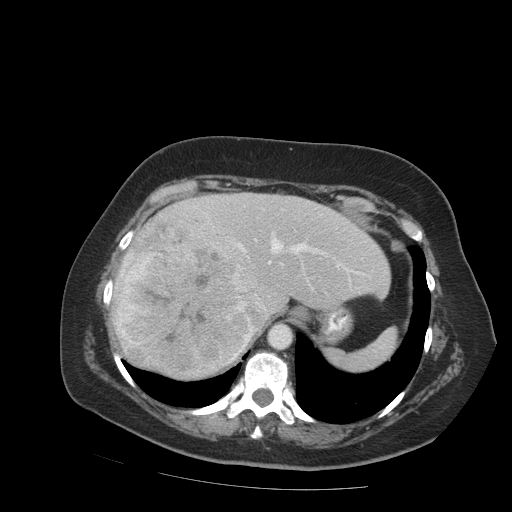
Contrast-enhanced abdominal CT (liver protocol), one axial slice. Slice 67 of 99 in the series (ordered by position). Reconstruction kernel STANDARD. Soft-tissue window (W 400 / L 40 HU). 512 × 512 image matrix, field of view 400 × 400 mm. Case-level facts recorded for this patient, not image findings: diagnosis: hepatocellular carcinoma (patient treated with transarterial chemoembolisation; whether this scan precedes or follows treatment is not stated here); TNM stage (as recorded): Stage-IVB; Child-Pugh class: A.
Structures marked on this image (semi-automatic segmentation, software-assisted and operator-edited):
- abdominal aorta: bounding box (x1, y1, x2, y2) in pixels: (268, 324, 292, 348)
- liver parenchyma outside the tumour (the mass and vessels are separate outlines, so this box may not span the whole liver): (114, 192, 390, 352)
- mass: (110, 223, 262, 380)
- liver vessels: (235, 238, 360, 274)